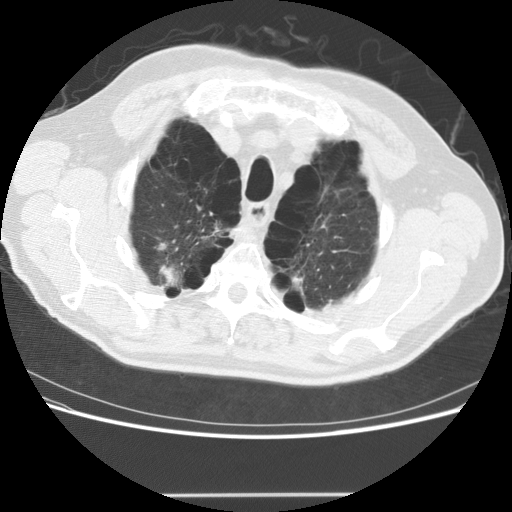
Low-dose screening chest CT, one axial slice. Position 121 of 151 along the scan axis. Reconstruction kernel STANDARD. 120 kVp. Lung window (W 1500 / L -600 HU). 512 × 512 image matrix, field of view 360 × 360 mm.
Annotated regions visible in this slice (outlined manually by an expert reader):
- lesion 1 (tumor, upper lobe of right lung): bounding box [x1, y1, x2, y2] px = [160, 263, 180, 288]